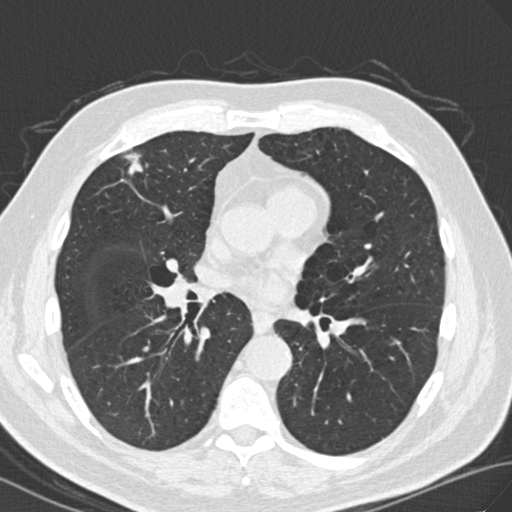
Low-dose screening chest CT, one axial slice; slice 85 of 171 in the series (ordered by position); 120 kVp; lung window (W 1500 / L -600 HU); 2 mm slice thickness; 512 × 512 image matrix, field of view 352 × 352 mm.
Structures marked on this image (outlined manually by an expert reader):
- lesion 1 (tumor, upper lobe of right lung): bounding box [x1, y1, x2, y2] px = [124, 153, 143, 175]